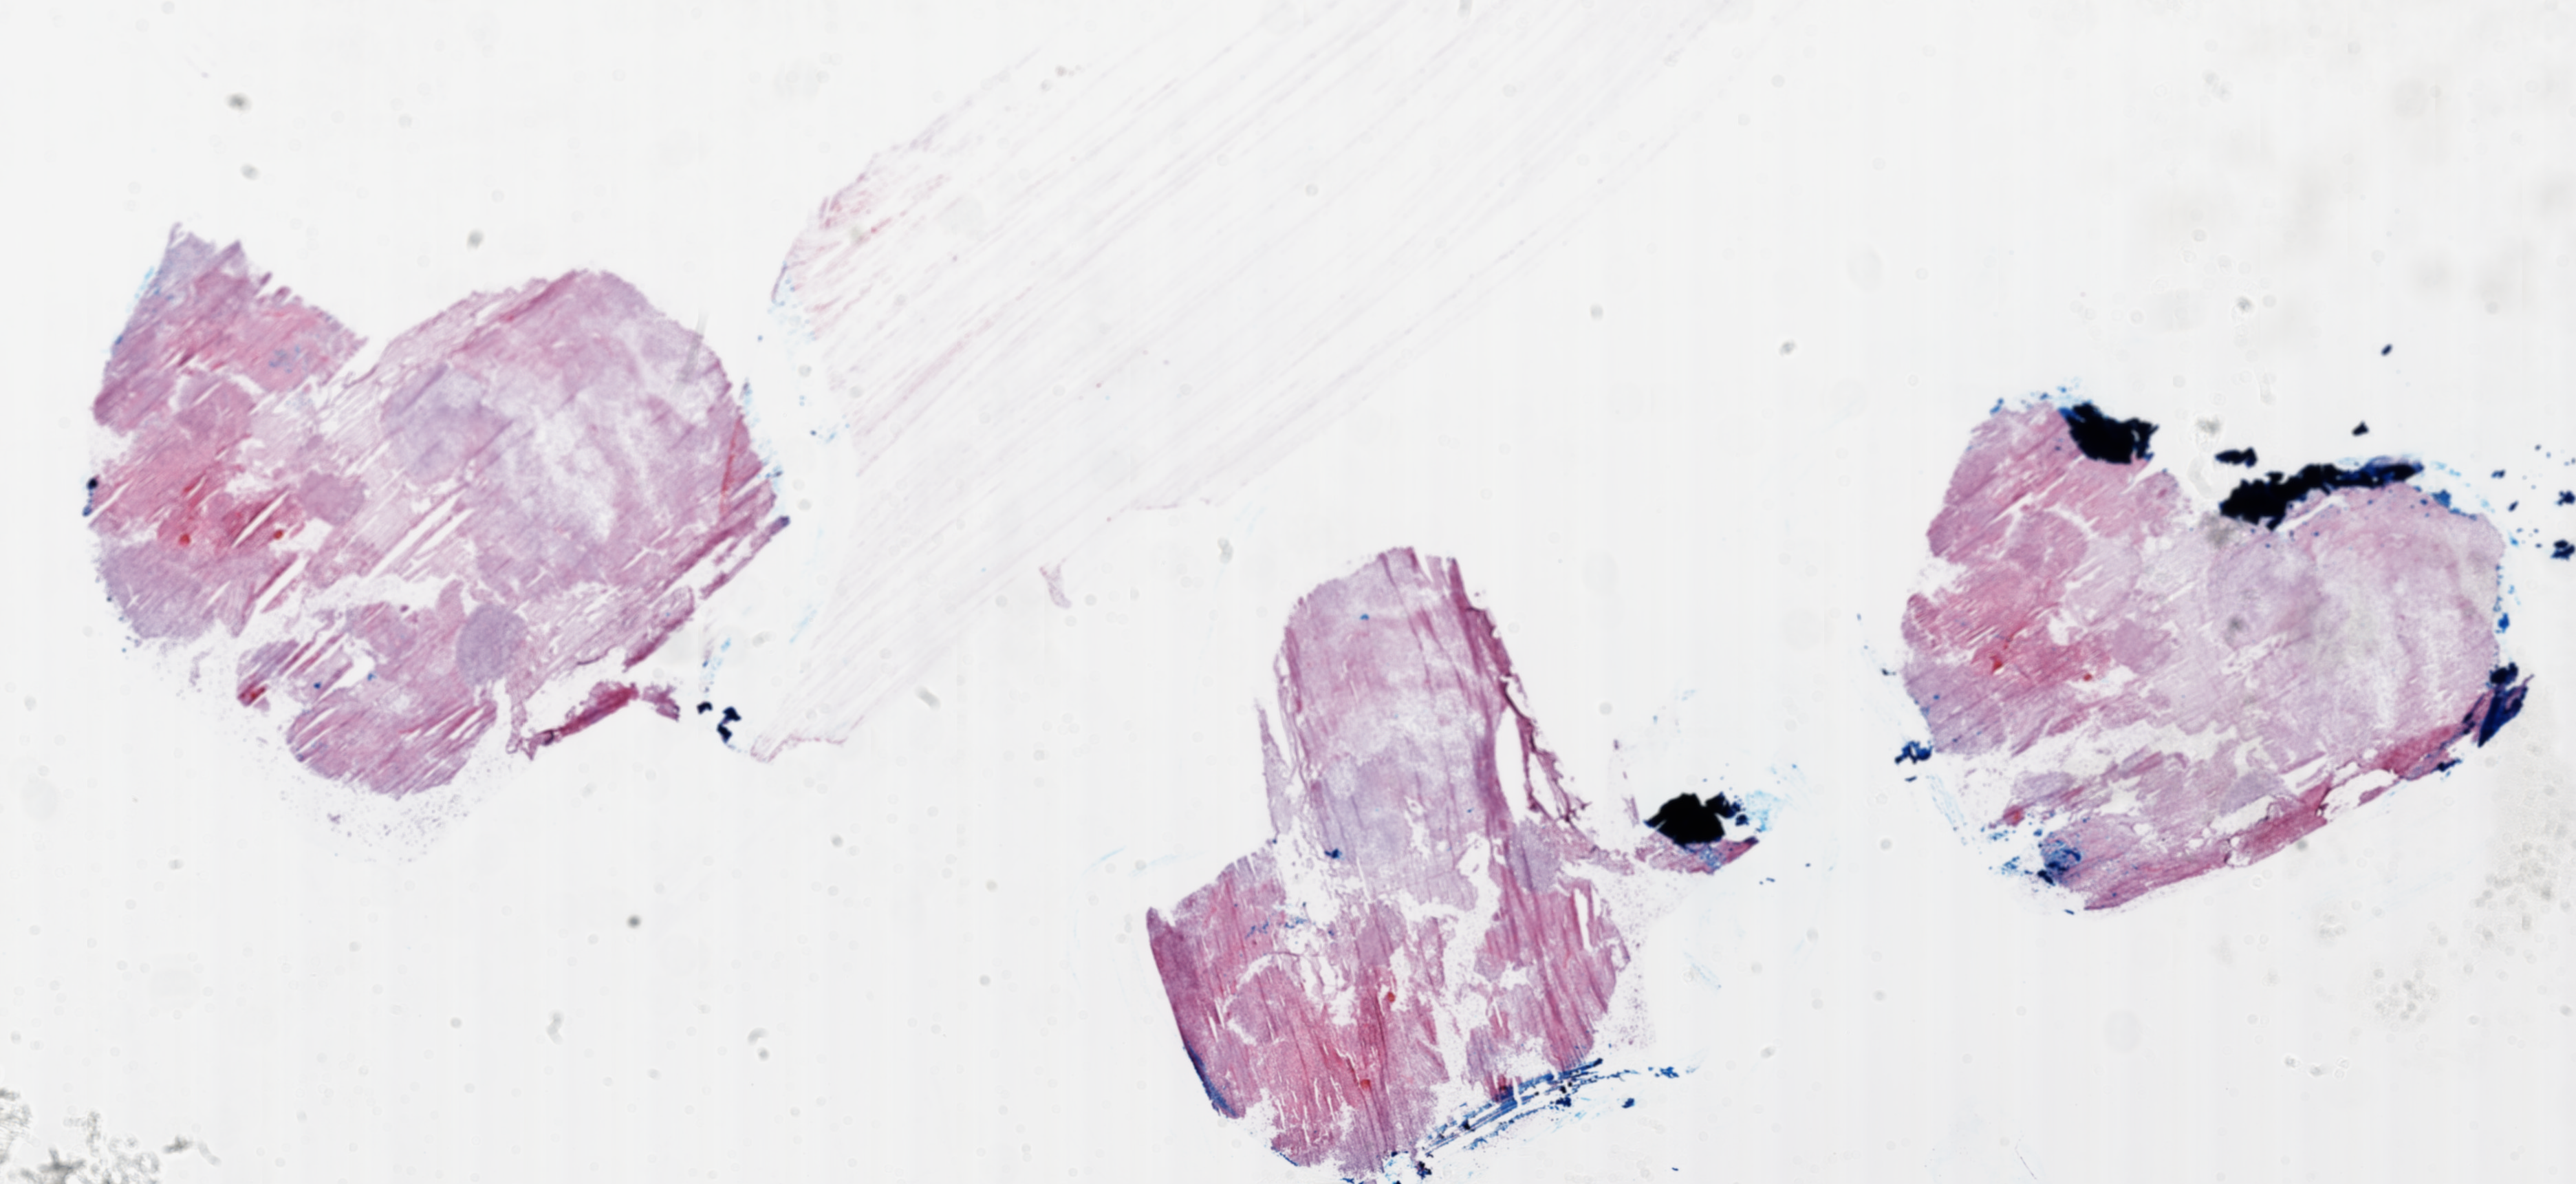
Whole-slide histology image, Hematoxylin and eosin (H&E) stained, low-resolution overview of the scanned area, about 30.0 x 13.8 mm (acquisition: 20x scan); frozen section; sample: primary tumour, brain. Patient: female, age at initial diagnosis 72 years. Slide review estimates, as recorded: tumour cells 10%, tumour nuclei 100%, normal cells 0%, stromal cells 0%, necrosis 90%.
Diagnosis: Glioblastoma.